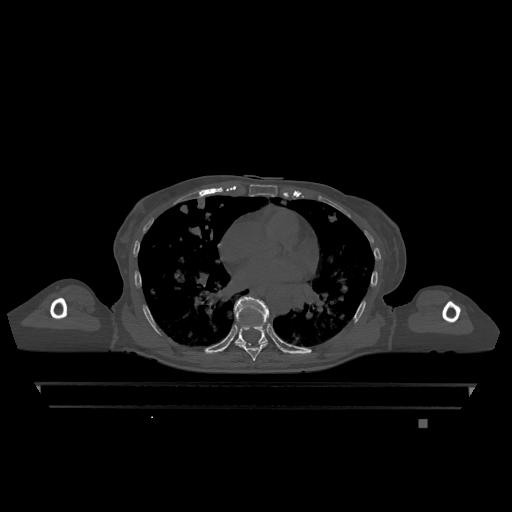
CT including the spine, one axial slice. Slice 717 of 1317 in the series (ordered by position). Bone window (W 1800 / L 400 HU). 0.5 mm slice thickness. 512 × 512 image matrix, field of view 500 × 500 mm. Patient: female, 74 years. Case-level facts recorded for this patient, not image findings: primary cancer: lung; vertebrae with lytic lesions (as recorded): T1, T4, T5, T6, L4, L5.
Structures marked on this image (semi-automatically segmented with operator editing):
- T7 vertebra: bounding box [x1, y1, x2, y2] px = [237, 343, 268, 361]
- T9 vertebra: [234, 297, 269, 345]